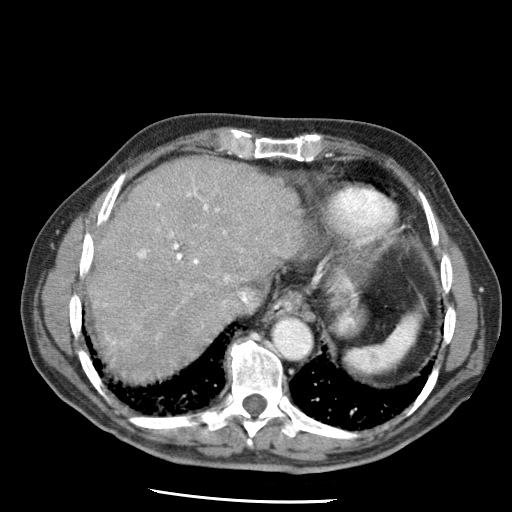
Contrast-enhanced abdominal CT (liver protocol), one axial slice; position 55 of 79 along the scan axis; soft-tissue window (W 400 / L 40 HU); 512 × 512 image matrix, field of view 320 × 320 mm. Case-level facts recorded for this patient, not image findings: diagnosis: hepatocellular carcinoma (patient treated with transarterial chemoembolisation; whether this scan precedes or follows treatment is not stated here); TNM stage (as recorded): Stage-IIIA; Child-Pugh class: A; tumour size: 7 cm.
Annotated regions visible in this slice (semi-automatically segmented with operator editing):
- abdominal aorta: bounding box (x1, y1, x2, y2) in pixels: (275, 320, 311, 358)
- liver parenchyma outside the tumour (the mass and vessels are separate outlines, so this box may not span the whole liver): (88, 158, 304, 380)
- liver vessels: (104, 185, 276, 345)